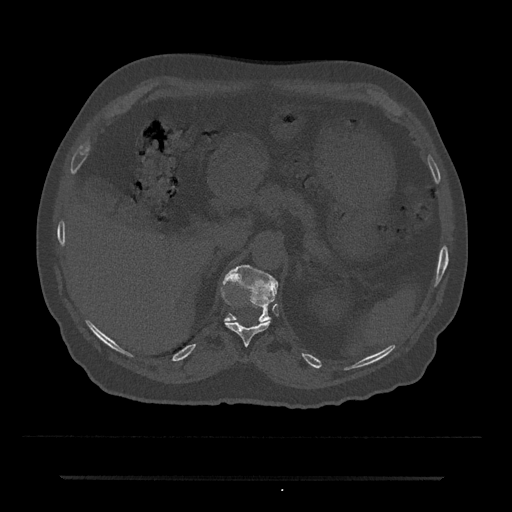
CT including the spine, one axial slice; slice 163 of 797 in the series (ordered by position); reconstruction kernel Br40s/3; 120 kVp; bone window (W 1800 / L 400 HU); 0.5 mm slice thickness; 512 × 512 image matrix, field of view 437 × 437 mm. Male patient, age 69 years. Case-level facts recorded for this patient, not image findings: primary cancer: prostate.
Structures marked on this image (semi-automatic segmentation, software-assisted and operator-edited):
- T11 vertebra: bounding box [x1, y1, x2, y2] px = [225, 321, 270, 346]
- T12 vertebra: [225, 265, 279, 322]